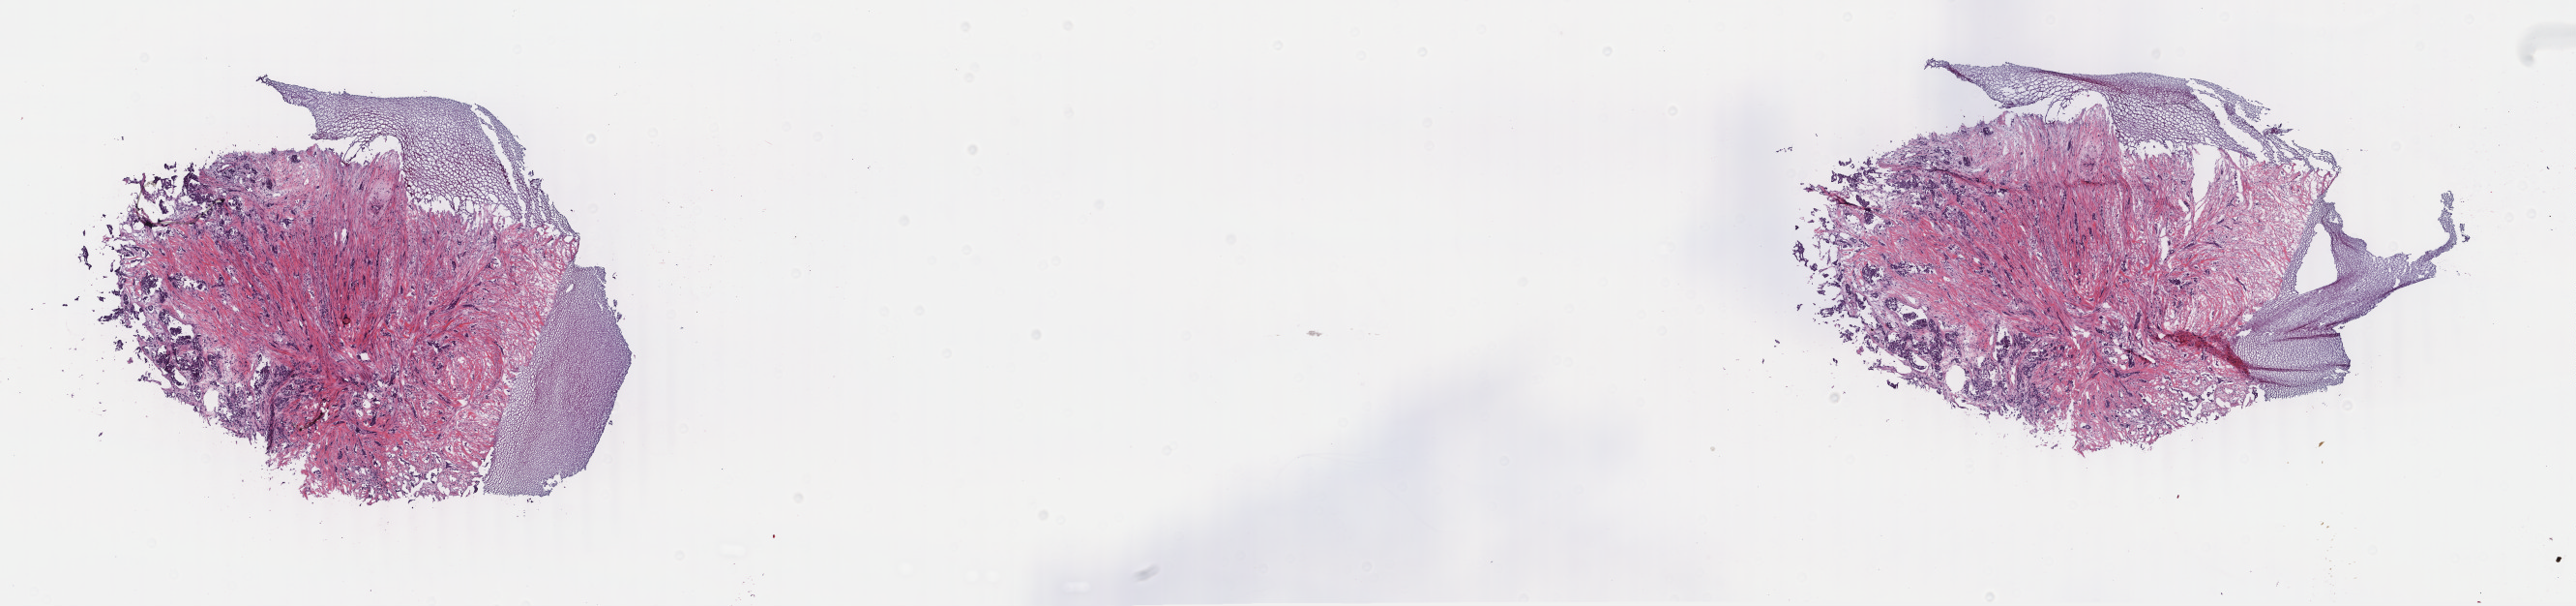
Hematoxylin and eosin (H&E) stained whole-slide image, low-resolution overview of the scanned area, about 21.2 x 5.0 mm (slide scanned at 40x). Frozen section from the top of the tissue portion. Primary tumour sample from the breast. Female, age 51 years at initial diagnosis. Composition of this section per pathologist review: tumour cells 30%, tumour nuclei 40%, normal cells 0%, stromal cells 70%, necrosis 0%. Inflammatory infiltration, as recorded: lymphocyte infiltration 0%, monocyte infiltration 0%, neutrophil infiltration 0%.
Pathologic diagnosis: Infiltrating duct carcinoma, NOS. TNM: T2 N0 (i-) M0. AJCC pathologic stage: IIA (6th edition).